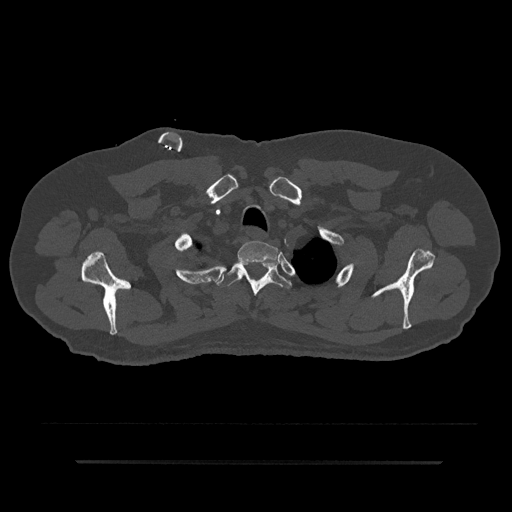
CT including the spine, one axial slice. Position 711 of 797 along the scan axis. Reconstruction kernel Br40s/3. 120 kVp. Bone window (W 1800 / L 400 HU). 0.5 mm slice thickness. 512 × 512 image matrix, field of view 464 × 464 mm. Patient: male, 59 years. From the clinical record (not read from this slice): primary cancer: bile ducts.
Outlined on this slice (semi-automatic segmentation, software-assisted and operator-edited):
- T1 vertebra: box from (x=237, y=241) to (x=278, y=266) px
- T2 vertebra: (x=216, y=262)–(x=292, y=296)